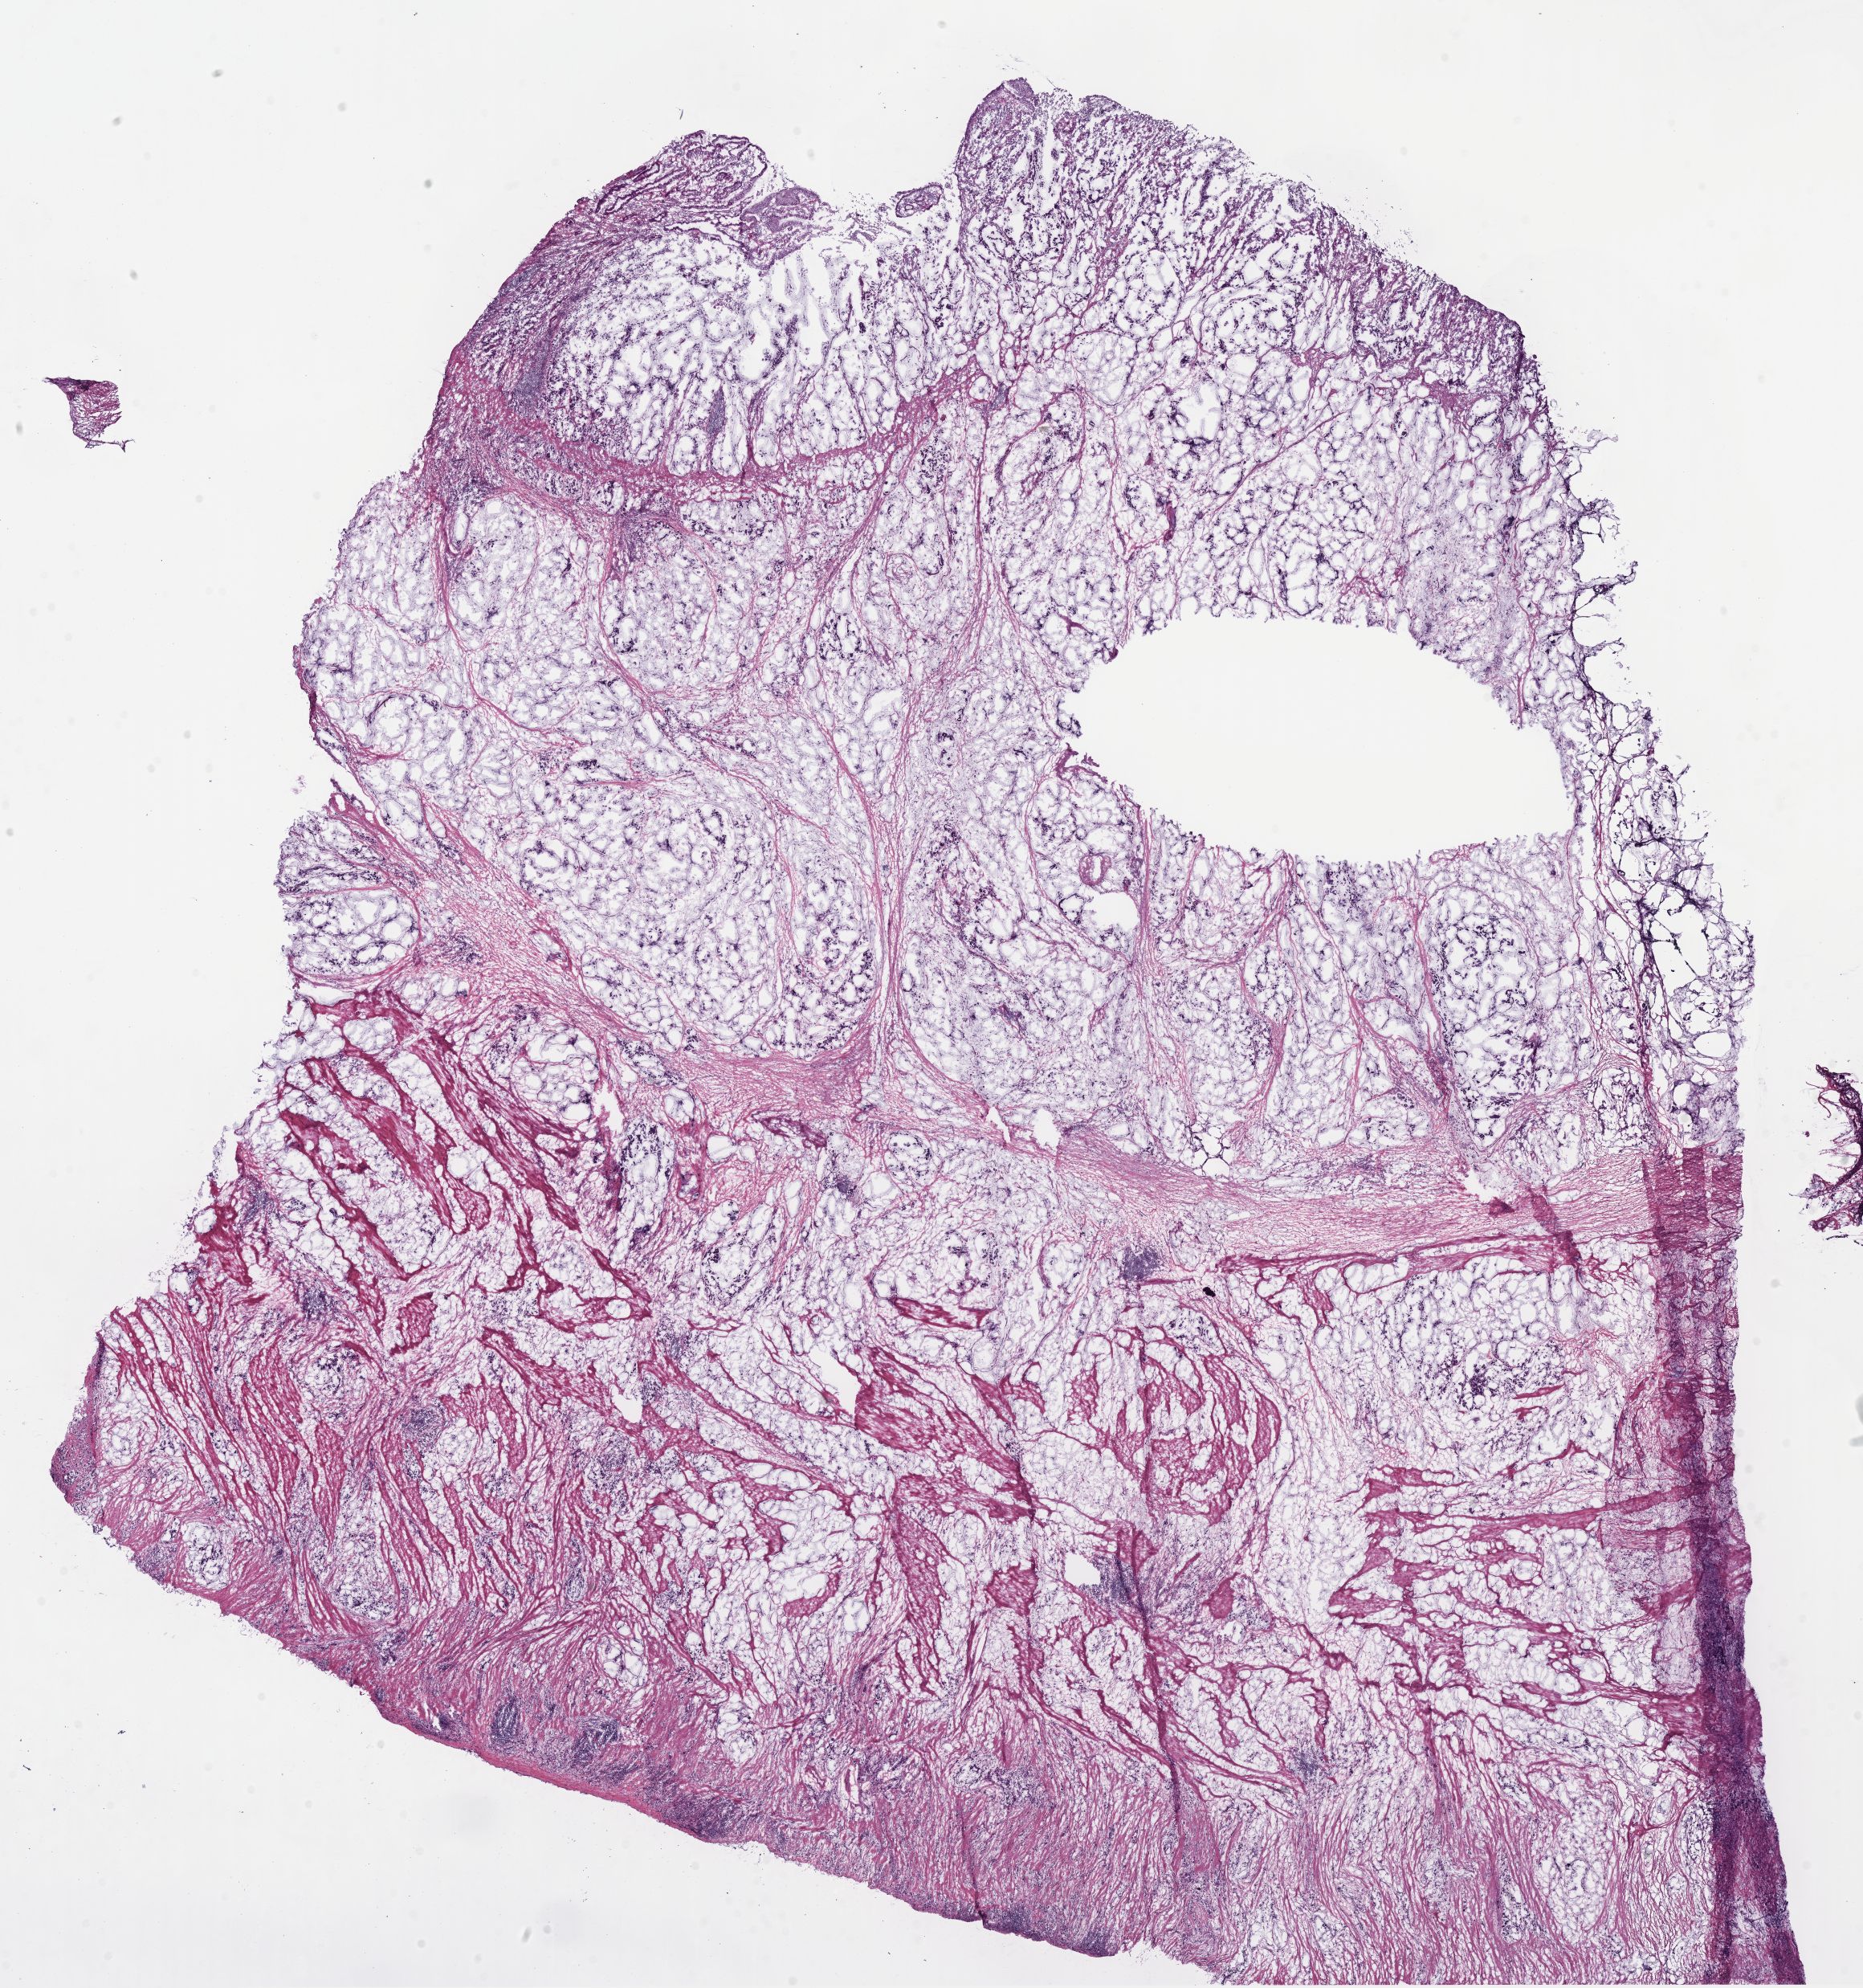
H&E-stained whole-slide image — low-resolution overview of the scanned area, about 18.3 x 19.5 mm (acquisition: 40x scan), frozen section from the bottom of the tissue portion, sample: primary tumour, stomach. Female patient; age at initial diagnosis 72 years. Histologic grade: G3 (poorly differentiated). Composition of this section per pathologist review: tumour cells 100%, tumour nuclei 61%, normal cells 0%, stromal cells 0%, necrosis 0%. Infiltration values recorded for this section: lymphocyte infiltration 15%, monocyte infiltration 0%, neutrophil infiltration 15%.
- lymph nodes positive (case pathology): 10 of 12 examined
- pathologic diagnosis: Mucinous adenocarcinoma (body of stomach)
- AJCC pathologic stage: IIIC (7th edition)